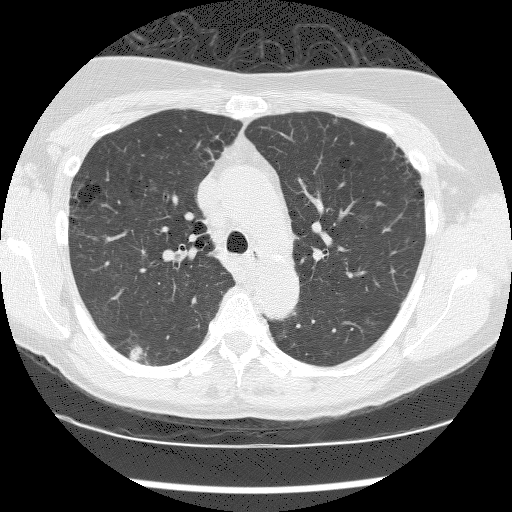
Low-dose screening chest CT, one axial slice; position 127 of 176 along the scan axis; 120 kVp; lung window (W 1500 / L -600 HU); 512 × 512 image matrix, field of view 320 × 320 mm.
Outlined on this slice (outlined manually by an expert reader):
- lesion 1 (tumor, lower lobe of right lung): bounding box [x1, y1, x2, y2] px = [129, 346, 147, 361]